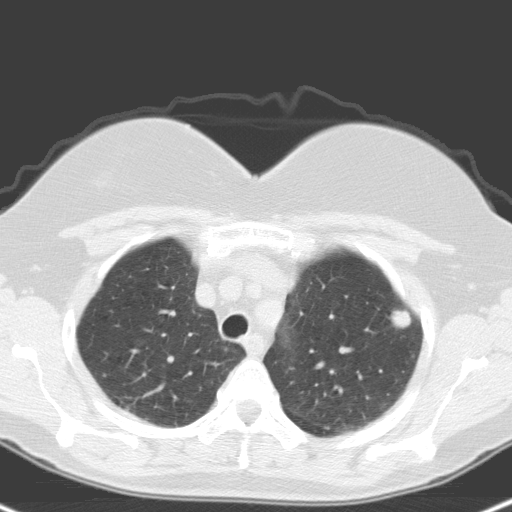
Low-dose screening chest CT, one axial slice; slice 125 of 148 in the series (ordered by position); 120 kVp; lung window (W 1500 / L -600 HU); 512 × 512 image matrix, field of view 314 × 314 mm.
Structures marked on this image (manually delineated by an expert):
- lesion 1 (tumor, upper lobe of left lung): bounding box <390,309,412,329> (left, top, right, bottom; pixels)